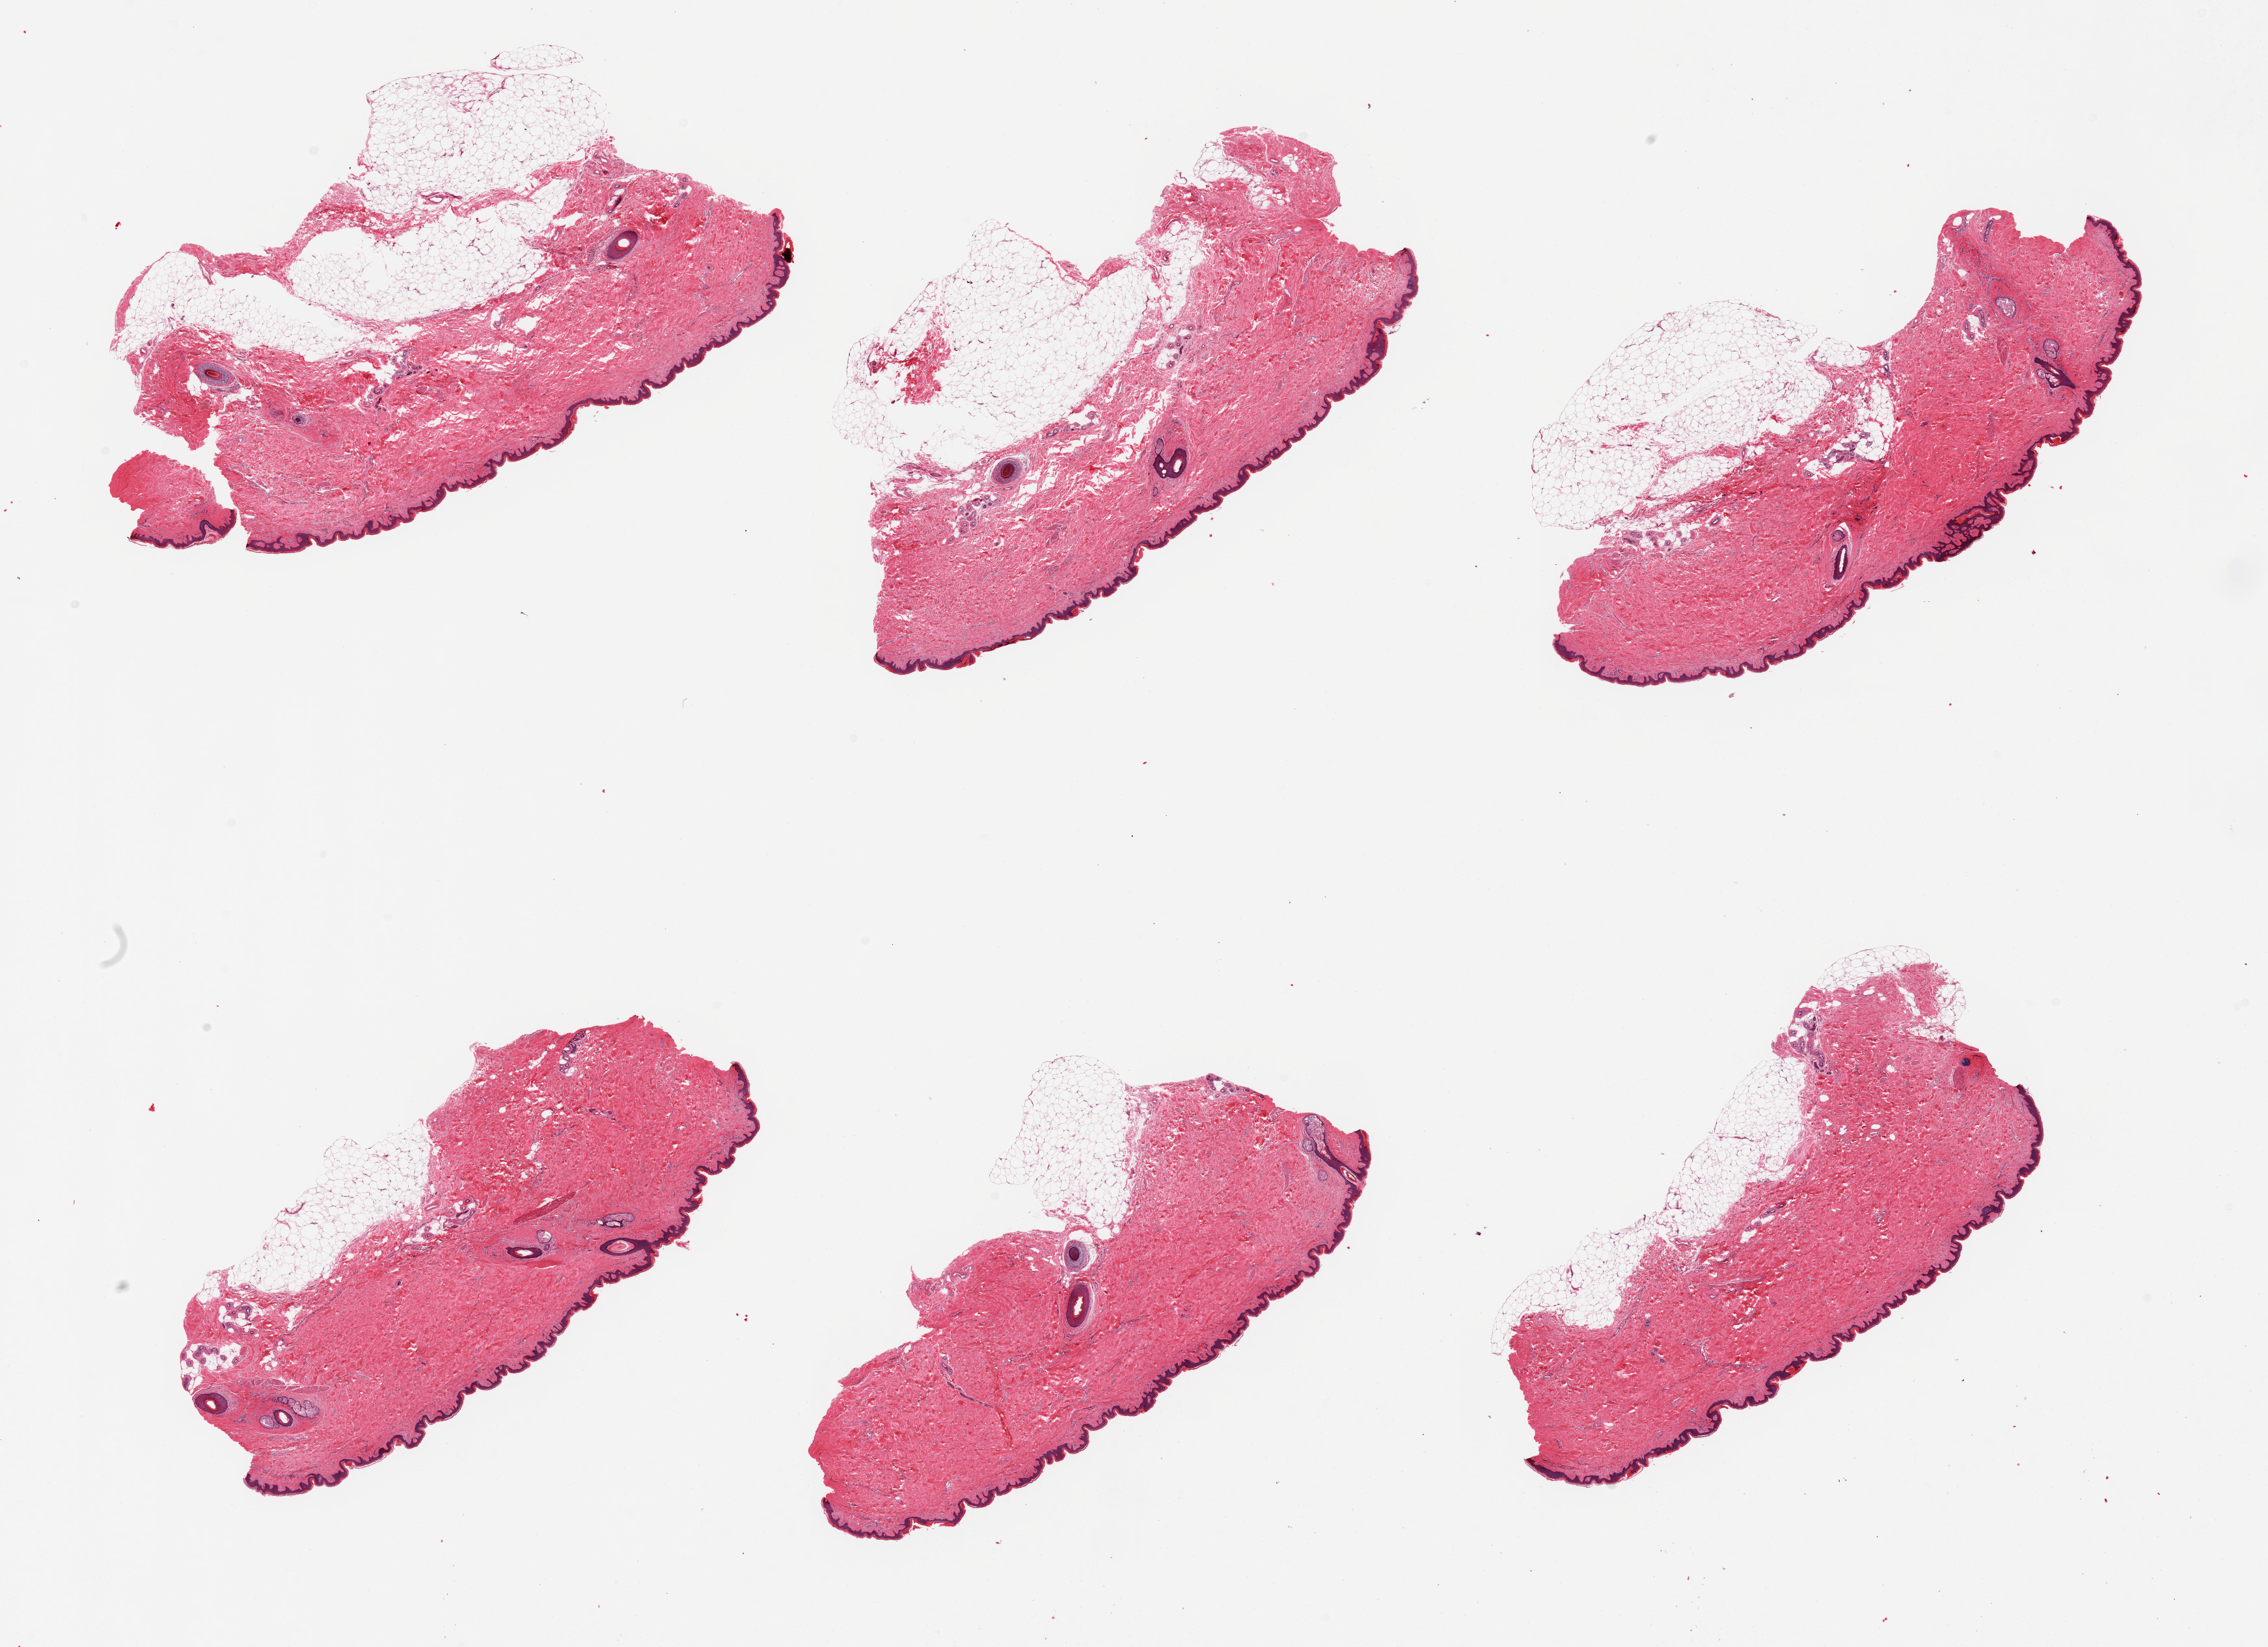
Hematoxylin and eosin (H&E) whole-slide image, a low-resolution overview of the entire scanned area, about 27.6 x 20.0 mm. PAXgene-fixed paraffin-embedded (PFPE) section. Section of skin of suprapubic region (target tissue). Donor tissue sample. Donor sex: female.
* pathologist's review note for this sample: 6 pieces, substantial attached adipose tissue from 10-40%